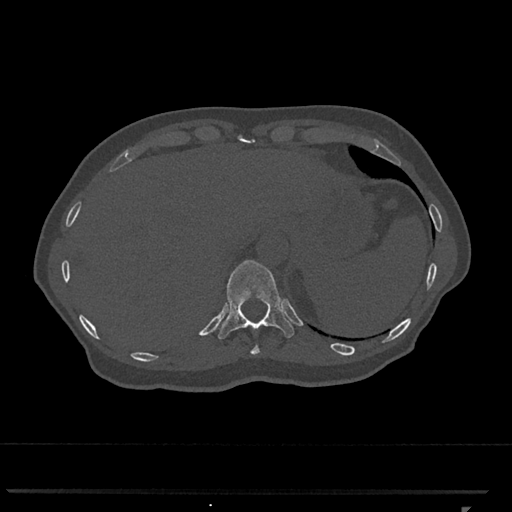
CT including the spine, one axial slice; 120 kVp; bone window (W 1800 / L 400 HU); 0.5 mm slice thickness; 512 × 512 image matrix, field of view 380 × 380 mm. Female patient, age 62 years. Case-level facts recorded for this patient, not image findings: primary cancer: renal.
Annotated regions visible in this slice (semi-automatic segmentation, software-assisted and operator-edited):
- T10 vertebra: bounding box <251,345,259,355> (left, top, right, bottom; pixels)
- T11 vertebra: <218,260,294,339>